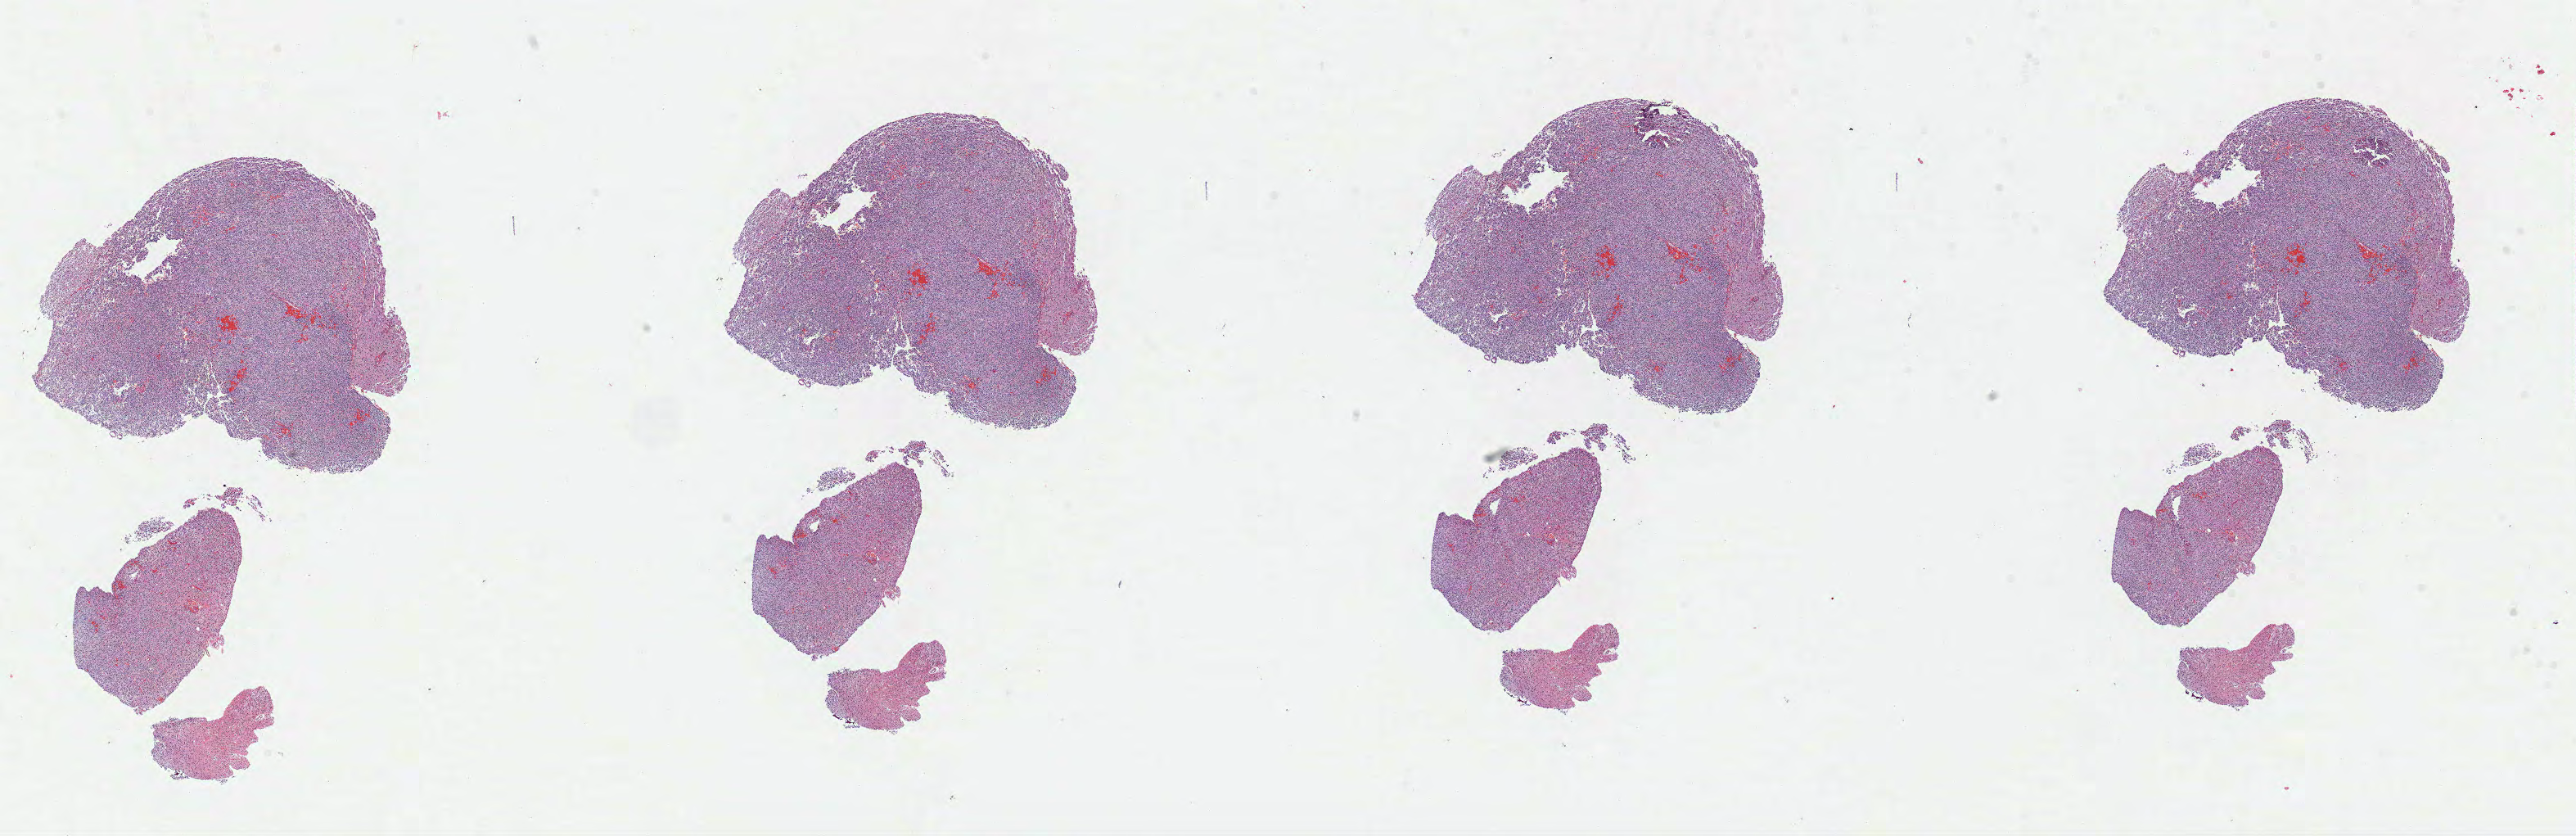
Whole-slide histology image, Hematoxylin and eosin (H&E) stained — shown as a low-resolution overview of the whole scanned area (about 25.4 x 8.2 mm, slide scanned at 40x), formalin-fixed paraffin-embedded (FFPE) diagnostic section, sample: primary tumour, brain. Female patient; age at initial diagnosis 62 years. Histologic grade: G2 (moderately differentiated).
Laterality: left. Pathologic diagnosis: Oligodendroglioma, NOS.